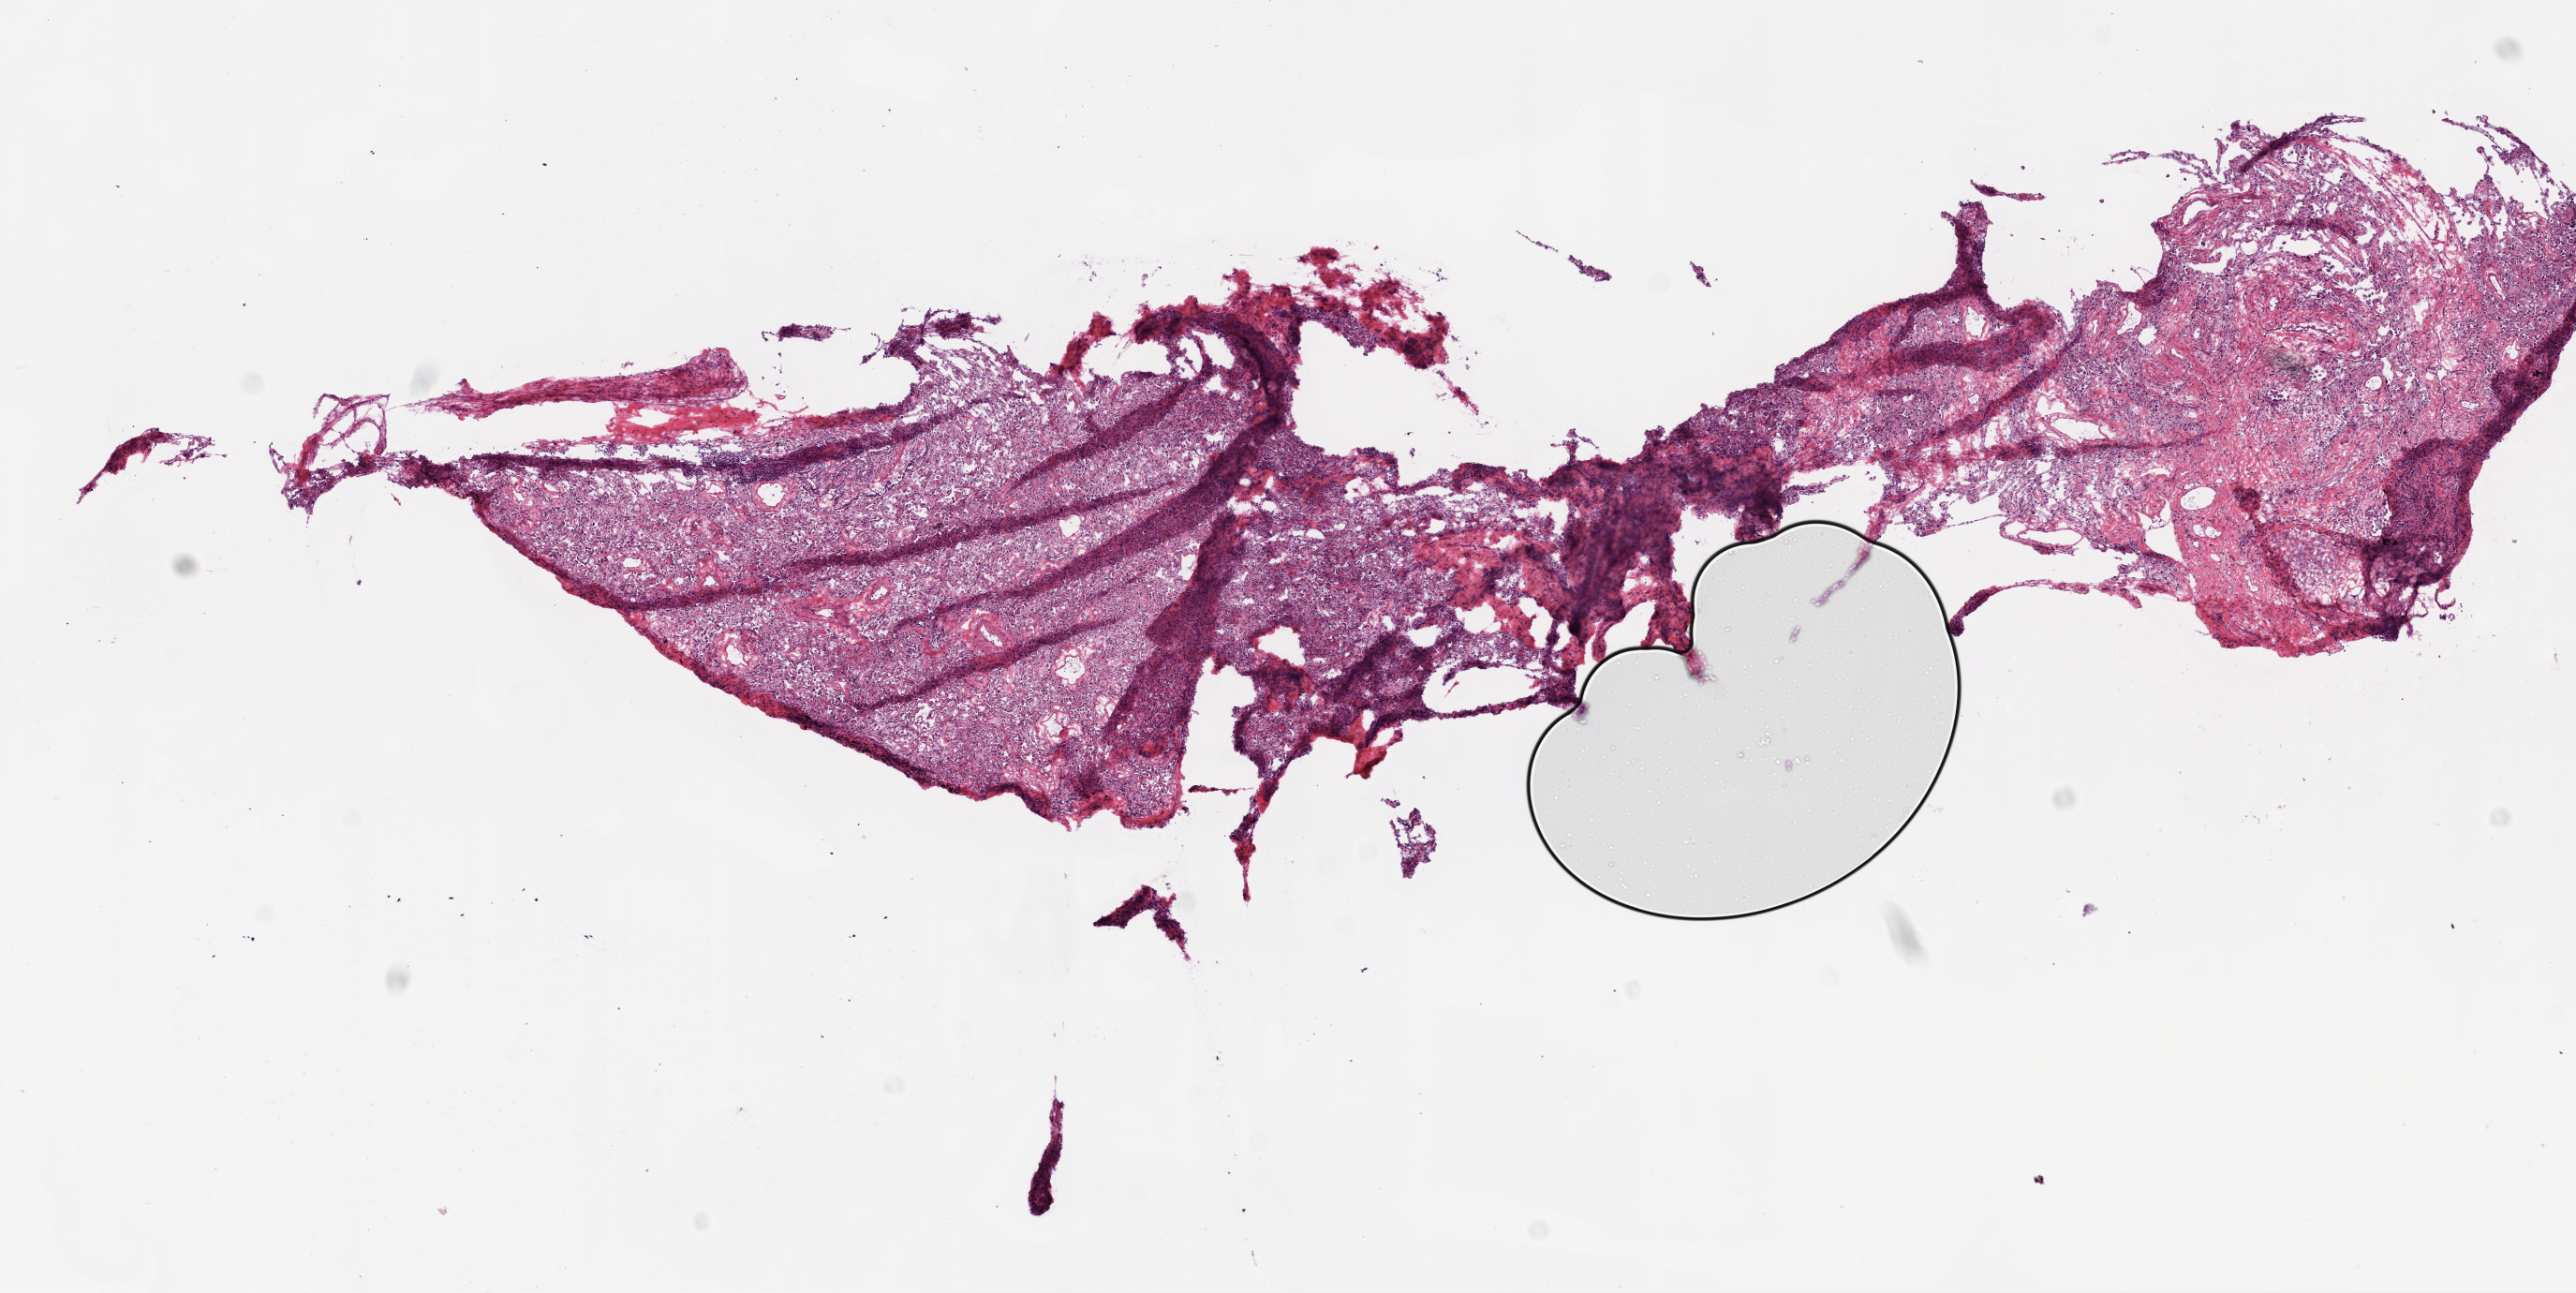
Whole-slide histology image, Hematoxylin and eosin (H&E) stained, a low-resolution overview of the entire scanned area, about 11.0 x 5.5 mm. Frozen section from the top of the tissue portion. Lung, solid tissue normal (non-tumour tissue) sample. Male, age 71 years at initial diagnosis.
- this section: solid tissue normal sample (biorepository sample class)
- patient diagnosis: Squamous cell carcinoma, NOS (lower lobe, lung)